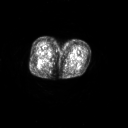
FDG PET of an extremity soft-tissue mass (from a PET/CT study), one axial slice; position 20 of 267 along the scan axis; 3.27 mm slice thickness; 128 × 128 image matrix, field of view 700 × 700 mm. Female patient, age 70 years. Case-level facts recorded for this patient, not image findings: histological type: synovial sarcoma; grade: intermediate; site of the primary tumour: right buttock.
Annotated regions visible in this slice (expert contour drawn on MRI and transferred to this co-registered scan by the dataset authors):
- gross tumour volume including surrounding oedema: bounding box [x1, y1, x2, y2] px = [35, 63, 39, 68]